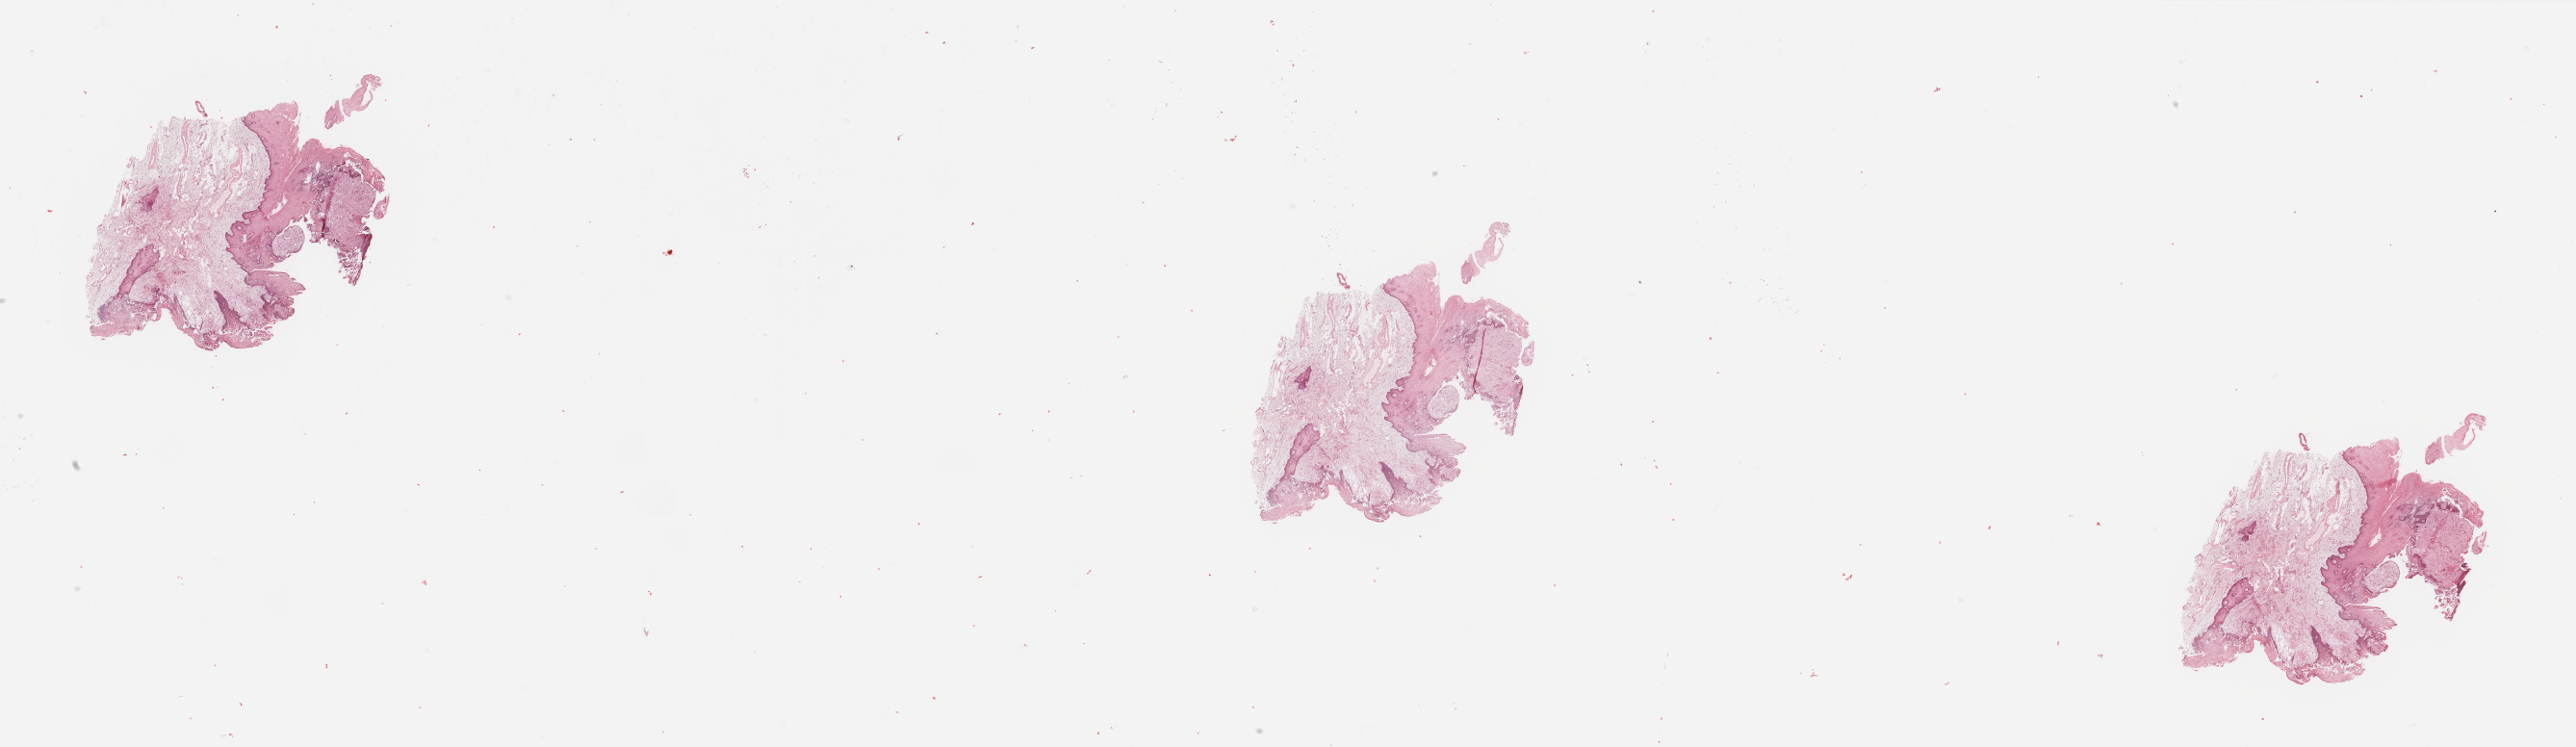
H&E whole-slide image, a low-resolution overview of the entire scanned area, about 42.3 x 12.3 mm; head and neck, normal (non-tumour) tissue. 65-year-old female patient.
This section: normal (non-tumour) tissue from the same patient. Patient diagnosis: Squamous cell carcinoma, NOS (floor of mouth, NOS).